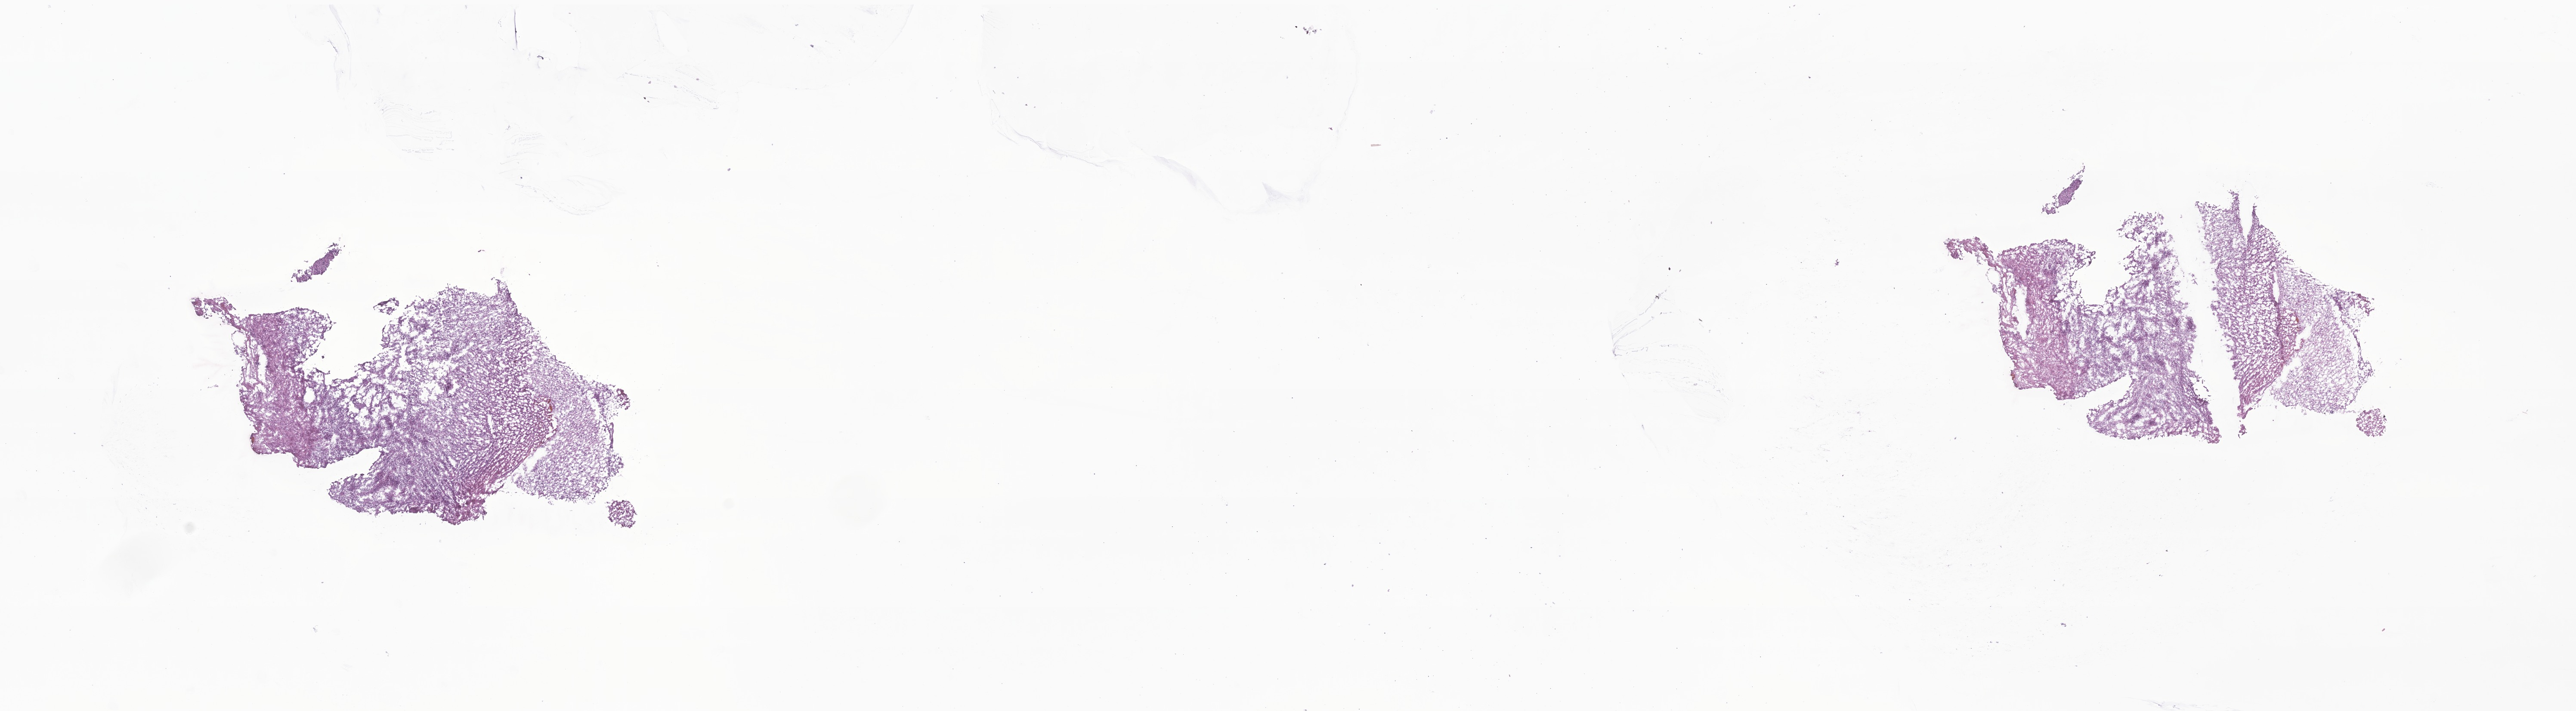
Digitized H&E-stained section of tumor tissue from the brain — whole scanned area (about 25.2 x 7.0 mm) shown as a low-resolution overview. Frozen section (OCT-embedded). Patient male; age 317 months (26 years 5 months).
Diagnosis (ICD-O-3 morphology term): Astrocytoma, NOS.